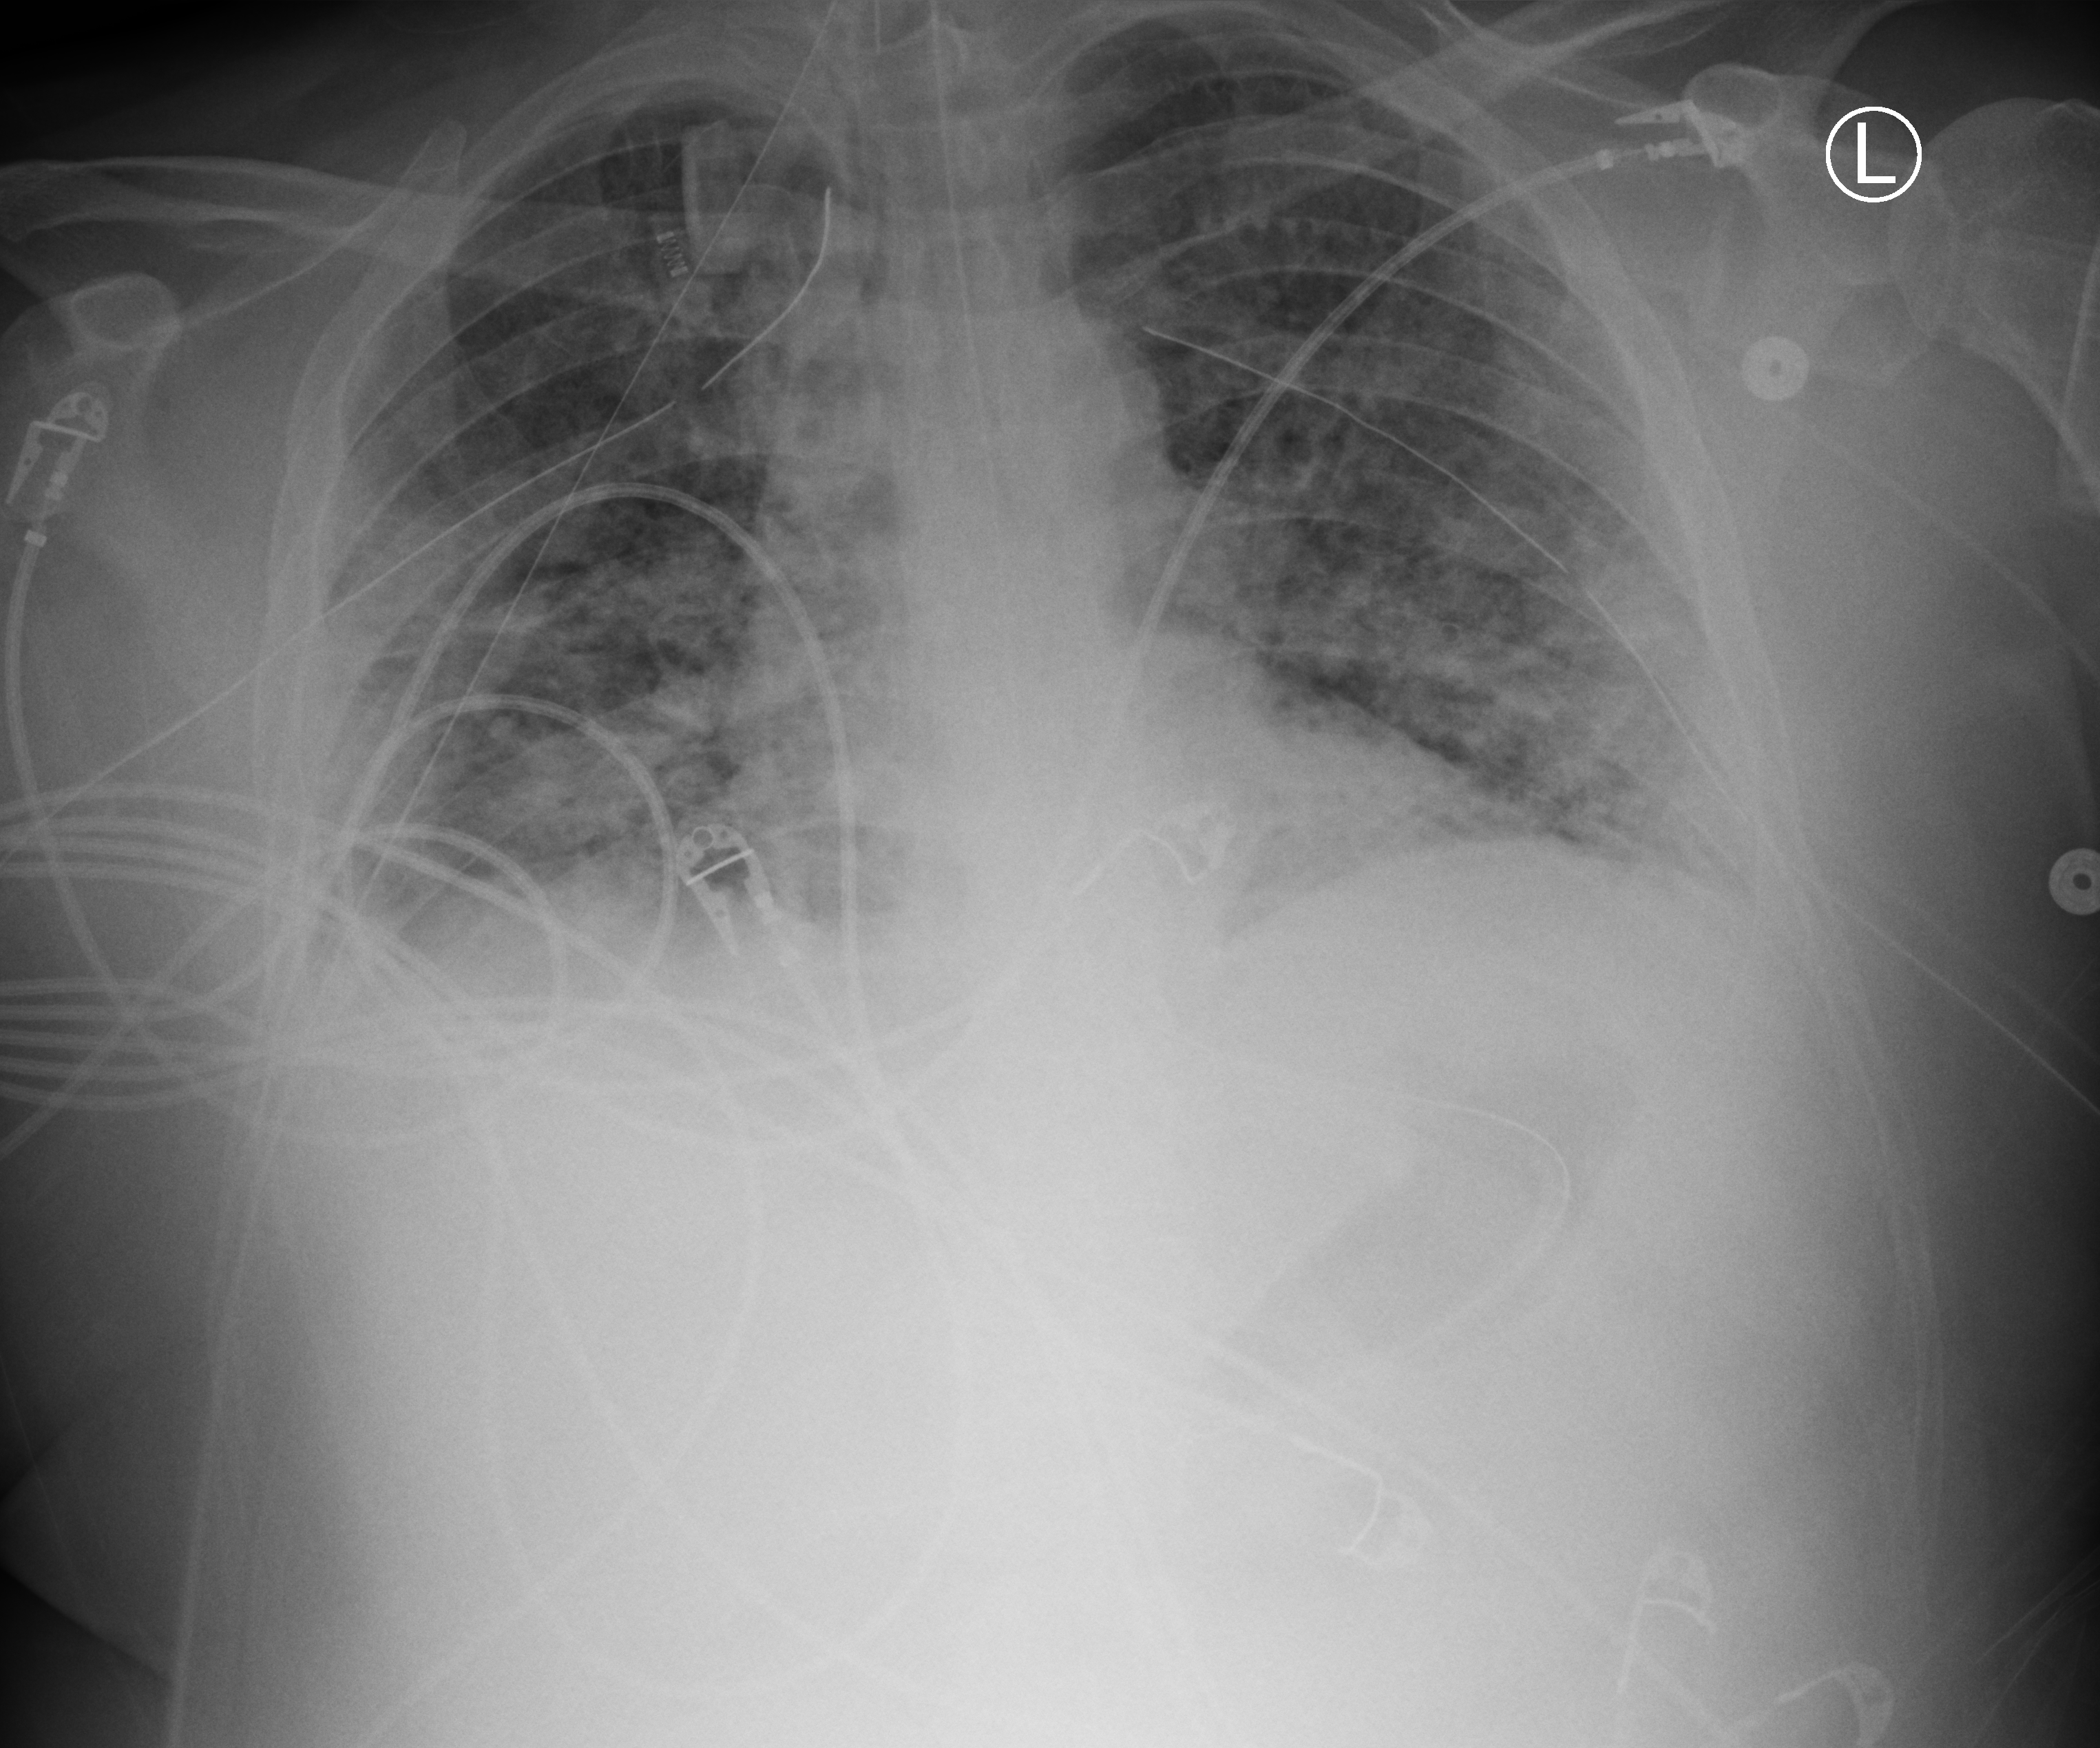
Portable chest radiograph; anteroposterior (AP) projection. Patient hospitalised with COVID-19; male, aged 18–59 years.
Hospital-stay facts (about this admission, not read from this image; timing relative to this image not recorded): chronic kidney disease (admission record): no.